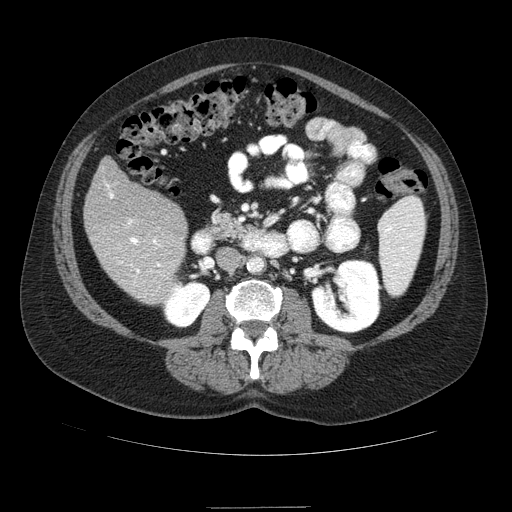
Contrast-enhanced abdominal CT (liver protocol), one axial slice. Slice 27 of 89 in the series (ordered by position). Reconstruction kernel STANDARD. 120 kVp. Soft-tissue window (W 400 / L 40 HU). 512 × 512 image matrix. From the clinical record (not read from this slice): diagnosis: hepatocellular carcinoma (patient treated with transarterial chemoembolisation; whether this scan precedes or follows treatment is not stated here); TNM stage (as recorded): Stage-IIIB; Child-Pugh class: A; tumour nodularity: multinodular.
Annotated regions visible in this slice (semi-automatic segmentation, software-assisted and operator-edited):
- liver parenchyma outside the tumour (the mass and vessels are separate outlines, so this box may not span the whole liver): bounding box (x1, y1, x2, y2) in pixels: (84, 157, 186, 303)
- liver vessels: (106, 184, 161, 274)